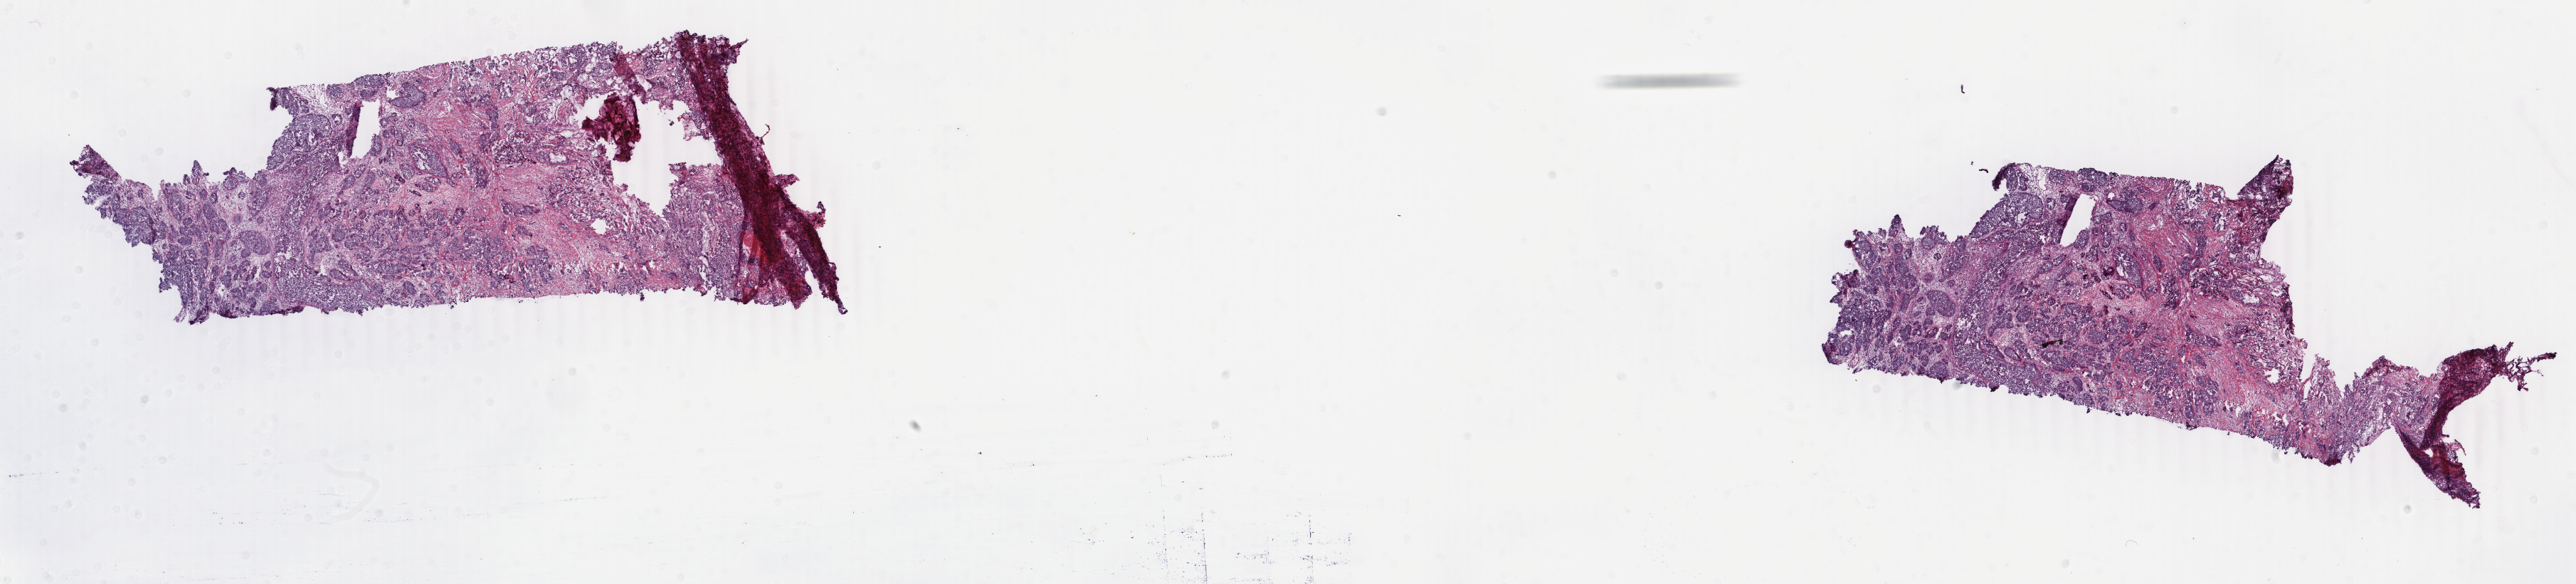
Whole-slide histology image, Hematoxylin and eosin (H&E) stained — a low-resolution overview of the entire scanned area, about 28.8 x 6.5 mm, frozen section from the bottom of the tissue portion, sample: primary tumour, breast. Female, age 36 years at initial diagnosis. Composition of this section per pathologist review: tumour cells 72%, tumour nuclei 85%, normal cells 0%, stromal cells 23%, necrosis 5%. Infiltration values recorded for this section: lymphocyte infiltration 3%, monocyte infiltration 1%, neutrophil infiltration 0%.
- lymph nodes positive (case pathology): 4 of 7 examined
- AJCC pathologic stage: IIIA (7th edition)
- laterality: left
- diagnosis: Infiltrating duct carcinoma, NOS